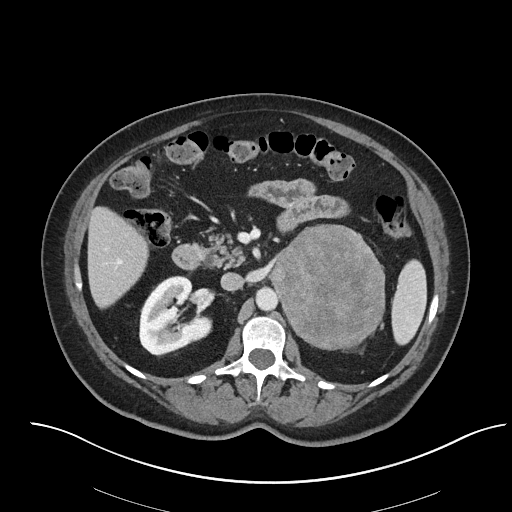
Contrast-enhanced abdominal CT, one axial slice. Position 40 of 92 along the scan axis. 120 kVp. Intravenous contrast given. Soft-tissue window (W 400 / L 40 HU). 512 × 512 image matrix, field of view 440 × 440 mm. Female patient, age 53 years. Case-level facts recorded for this patient, not image findings: diagnosis: adrenocortical carcinoma; tumour side: left adrenal; tumour size at pathology: 9 cm; Ki-67 index: 28 %; stage (as recorded): 2.
Structures marked on this image (semi-automatically segmented with operator editing):
- mass: box from (x=270, y=226) to (x=384, y=348) px